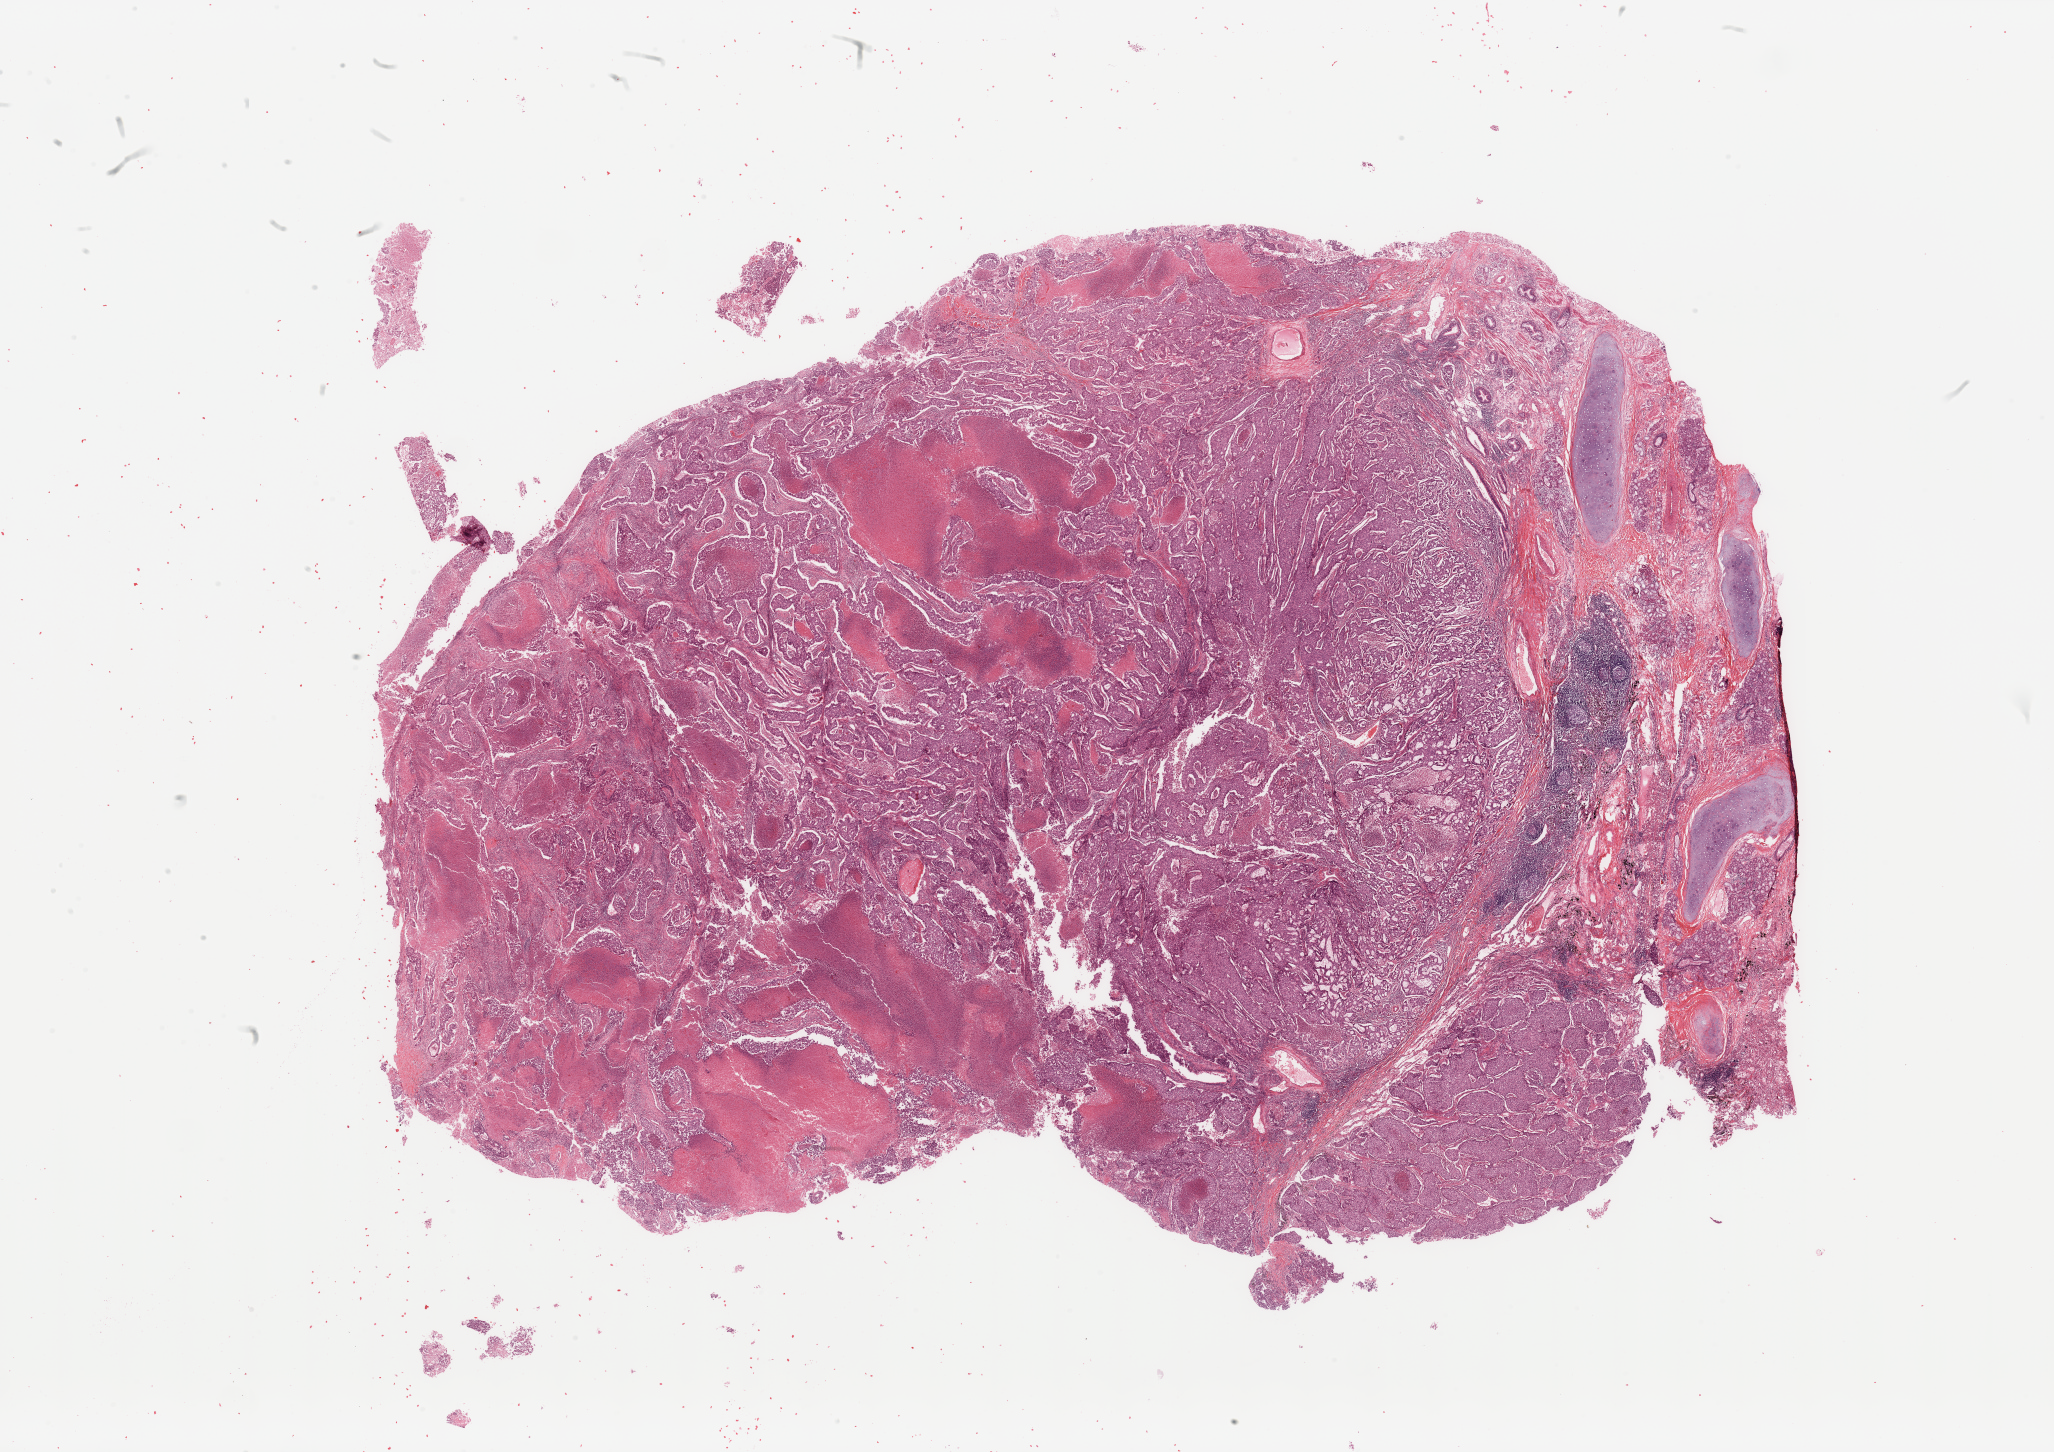
H&E whole-slide image — whole scanned area (about 32.5 x 23.0 mm, acquisition: 20x scan) shown as a low-resolution overview; tumour tissue sample, lung. Male, 45 y/o. Histologic grade: G3 (poorly differentiated).
- AJCC pathologic stage: IIB
- diagnosis: Adenocarcinoma, NOS